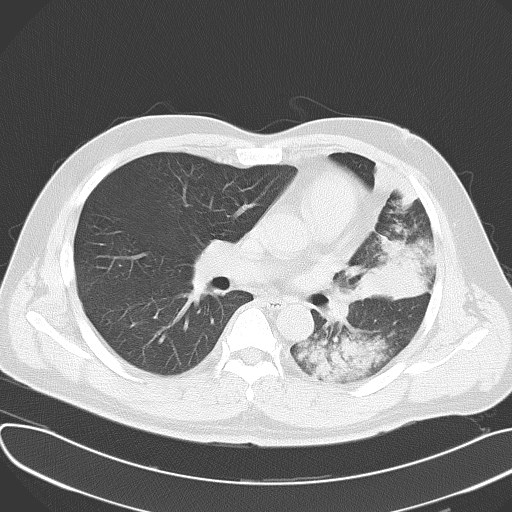
Chest CT, one axial slice; slice 35 of 62 in the series (ordered by position); reconstruction kernel B70f; 120 kVp; lung window (W 1500 / L -600 HU); 512 × 512 image matrix, field of view 377 × 377 mm. Patient: male, 48 years. From the clinical record (not read from this slice): clinical TNM (as recorded): T4 N0 M0.
Structures marked on this image (bounding box drawn by a radiologist):
- lung tumour (recorded histology: adenocarcinoma): bounding box [x1, y1, x2, y2] px = [351, 230, 428, 312]